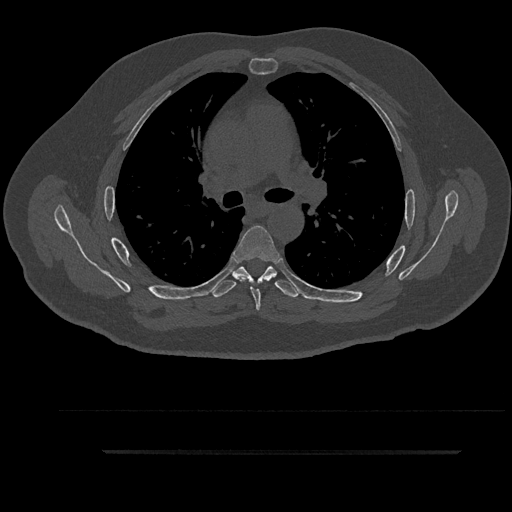
CT including the spine, one axial slice. Slice 607 of 797 in the series (ordered by position). Reconstruction kernel Br40s/3. Bone window (W 1800 / L 400 HU). 0.5 mm slice thickness. 512 × 512 image matrix, field of view 432 × 432 mm. Male patient, age 63 years. Case-level facts recorded for this patient, not image findings: primary cancer: renal; vertebrae with lytic lesions (as recorded): T8.
Annotated regions visible in this slice (semi-automatic segmentation, software-assisted and operator-edited):
- T5 vertebra: bounding box [x1, y1, x2, y2] px = [233, 225, 281, 311]
- T6 vertebra: [212, 266, 301, 298]